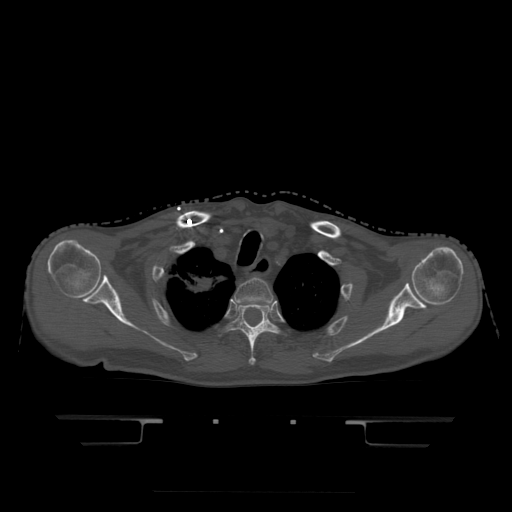
CT including the spine, one axial slice. Slice 375 of 522 in the series (ordered by position). Bone window (W 1800 / L 400 HU). 1.25 mm slice thickness. 512 × 512 image matrix, field of view 436 × 436 mm. Patient age 68 years. From the clinical record (not read from this slice): primary cancer: urothelial.
Structures marked on this image (semi-automatic segmentation, software-assisted and operator-edited):
- T2 vertebra: bounding box (x1, y1, x2, y2) in pixels: (234, 279, 274, 302)
- T3 vertebra: (229, 302, 278, 366)